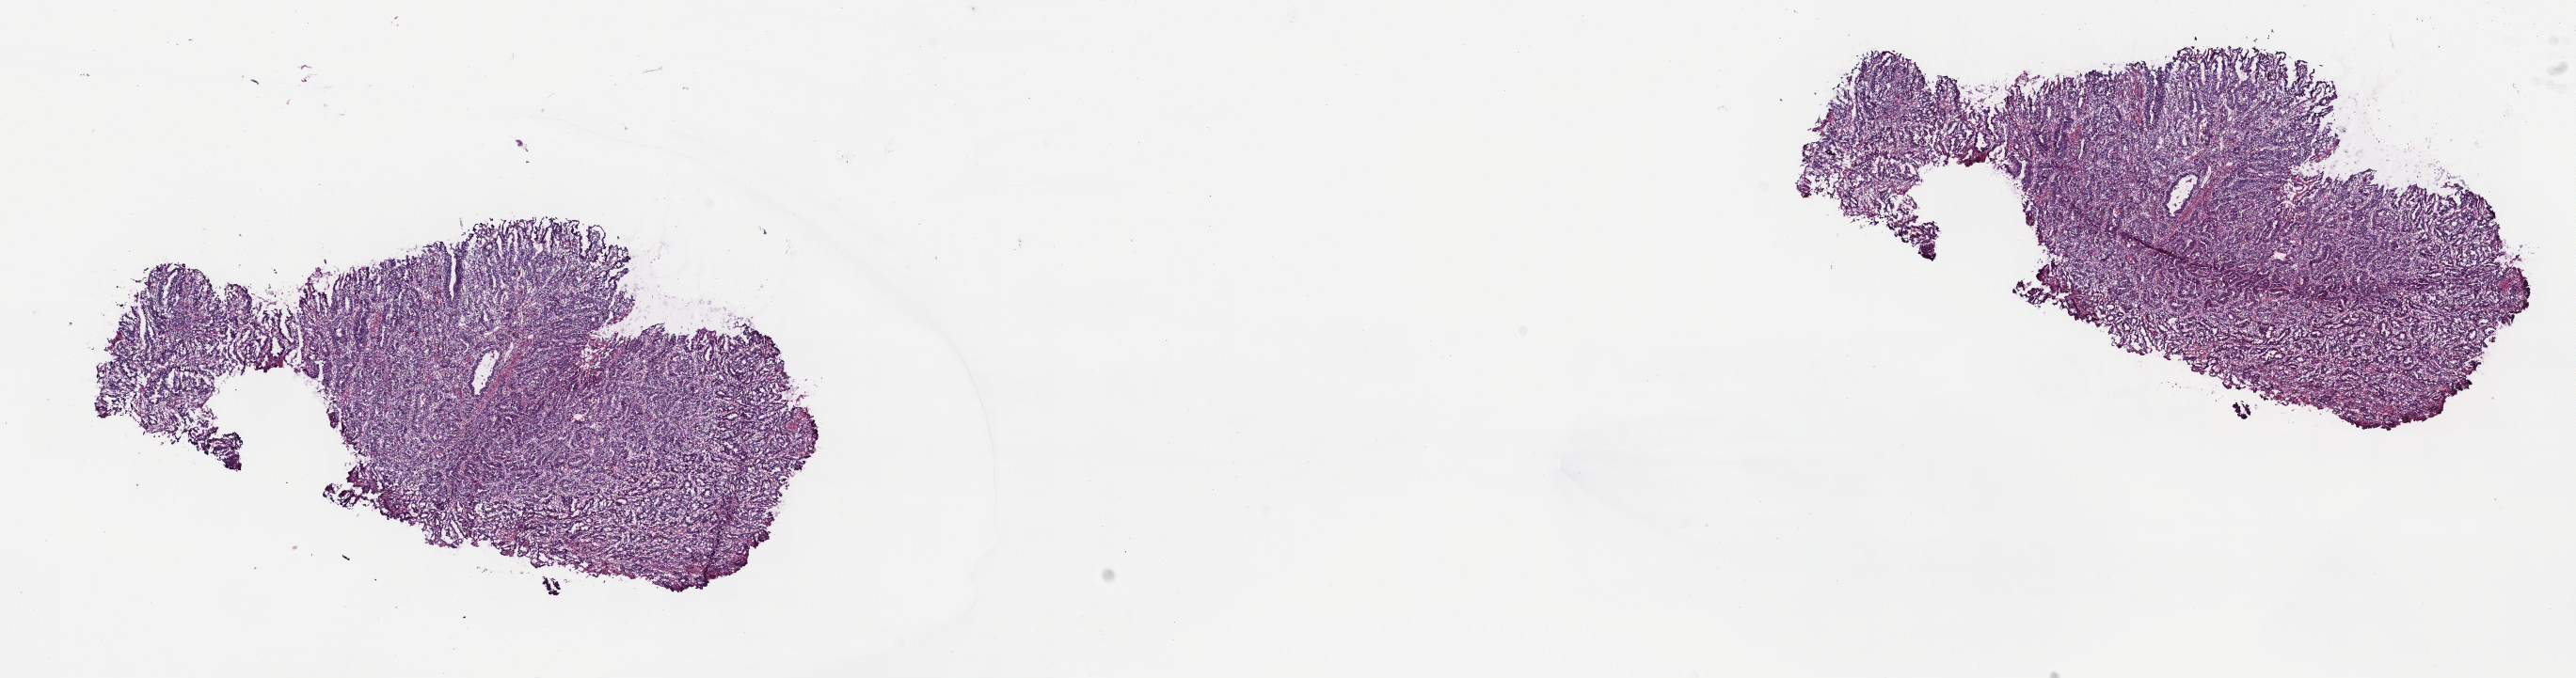
Whole-slide histology image, Hematoxylin and eosin (H&E) stained — shown as a low-resolution overview of the whole scanned area (about 22.1 x 5.8 mm). Frozen section from the top of the tissue portion. Stomach, primary tumour sample. Patient: male, age at initial diagnosis 74 years. Histologic grade: G2 (moderately differentiated). Composition of this section per pathologist review: tumour cells 82%, tumour nuclei 80%, normal cells 0%, stromal cells 15%, necrosis 3%. Inflammatory infiltration, as recorded: lymphocyte infiltration 15%, monocyte infiltration 2%, neutrophil infiltration 1%.
Histologic diagnosis: Adenocarcinoma, intestinal type (gastric antrum). AJCC pathologic stage: IIIC.